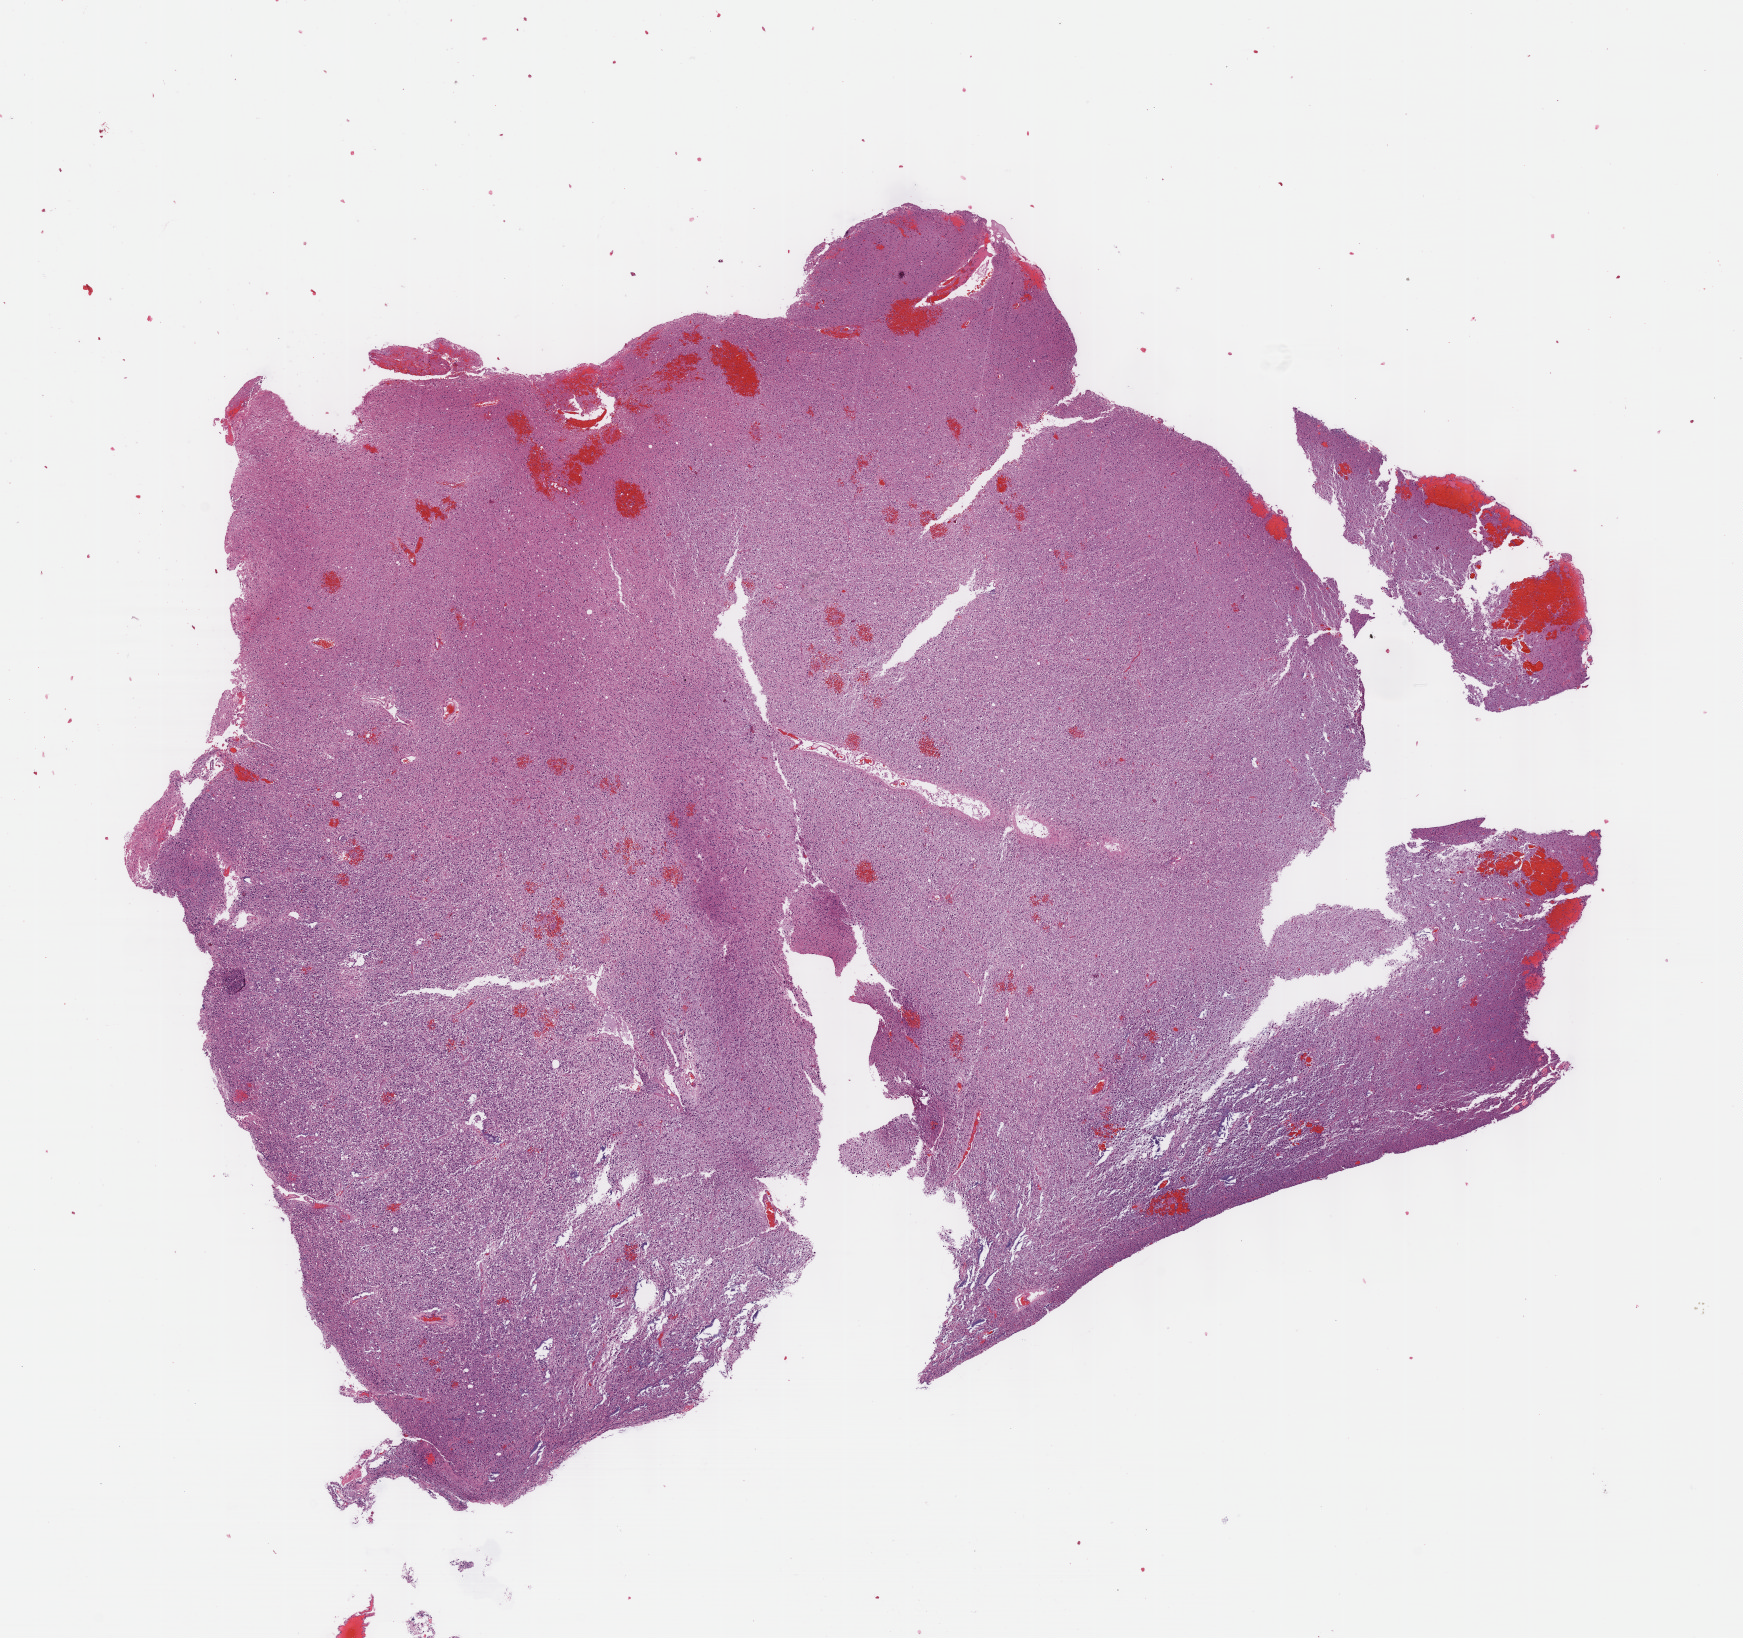
H&E whole-slide image, low-resolution overview of the scanned area, about 14.1 x 13.2 mm (acquisition: 40x scan), FFPE section, sample: primary tumour, brain. Patient: female, age at initial diagnosis 36 years. Histologic grade: G2 (moderately differentiated).
Laterality: left. Pathologic diagnosis: Astrocytoma, NOS.